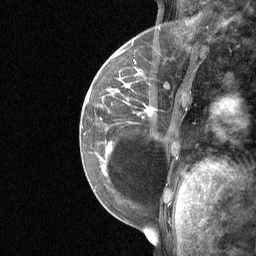
Breast MRI (dynamic contrast-enhanced), one sagittal slice; slice 18 of 64 in the series (ordered by position); dynamic contrast-enhanced study with each time point stored as its own series, time point 2 of 3 at this slice position (early post-contrast, ordered by acquisition time); 1.5 T; TE 4.8 ms, TR 27 ms; 2 mm slice thickness; 256 × 256 image matrix, field of view 200 × 200 mm. Patient: female, 34 years. From the clinical record (not read from this slice): setting: breast cancer imaged before/during neoadjuvant chemotherapy; receptor status: HR-positive, HER2-negative.
Outlined on this slice (semi-automatically segmented with operator editing):
- analysis volume of interest (the breast-tissue region the enhancement analysis was run in; not a lesion): bounding box (x1, y1, x2, y2) in pixels: (92, 50, 188, 185)
- tumour enhancement mask (voxels above the 90 % enhancement threshold inside the analysis volume of interest): (145, 106, 150, 112)